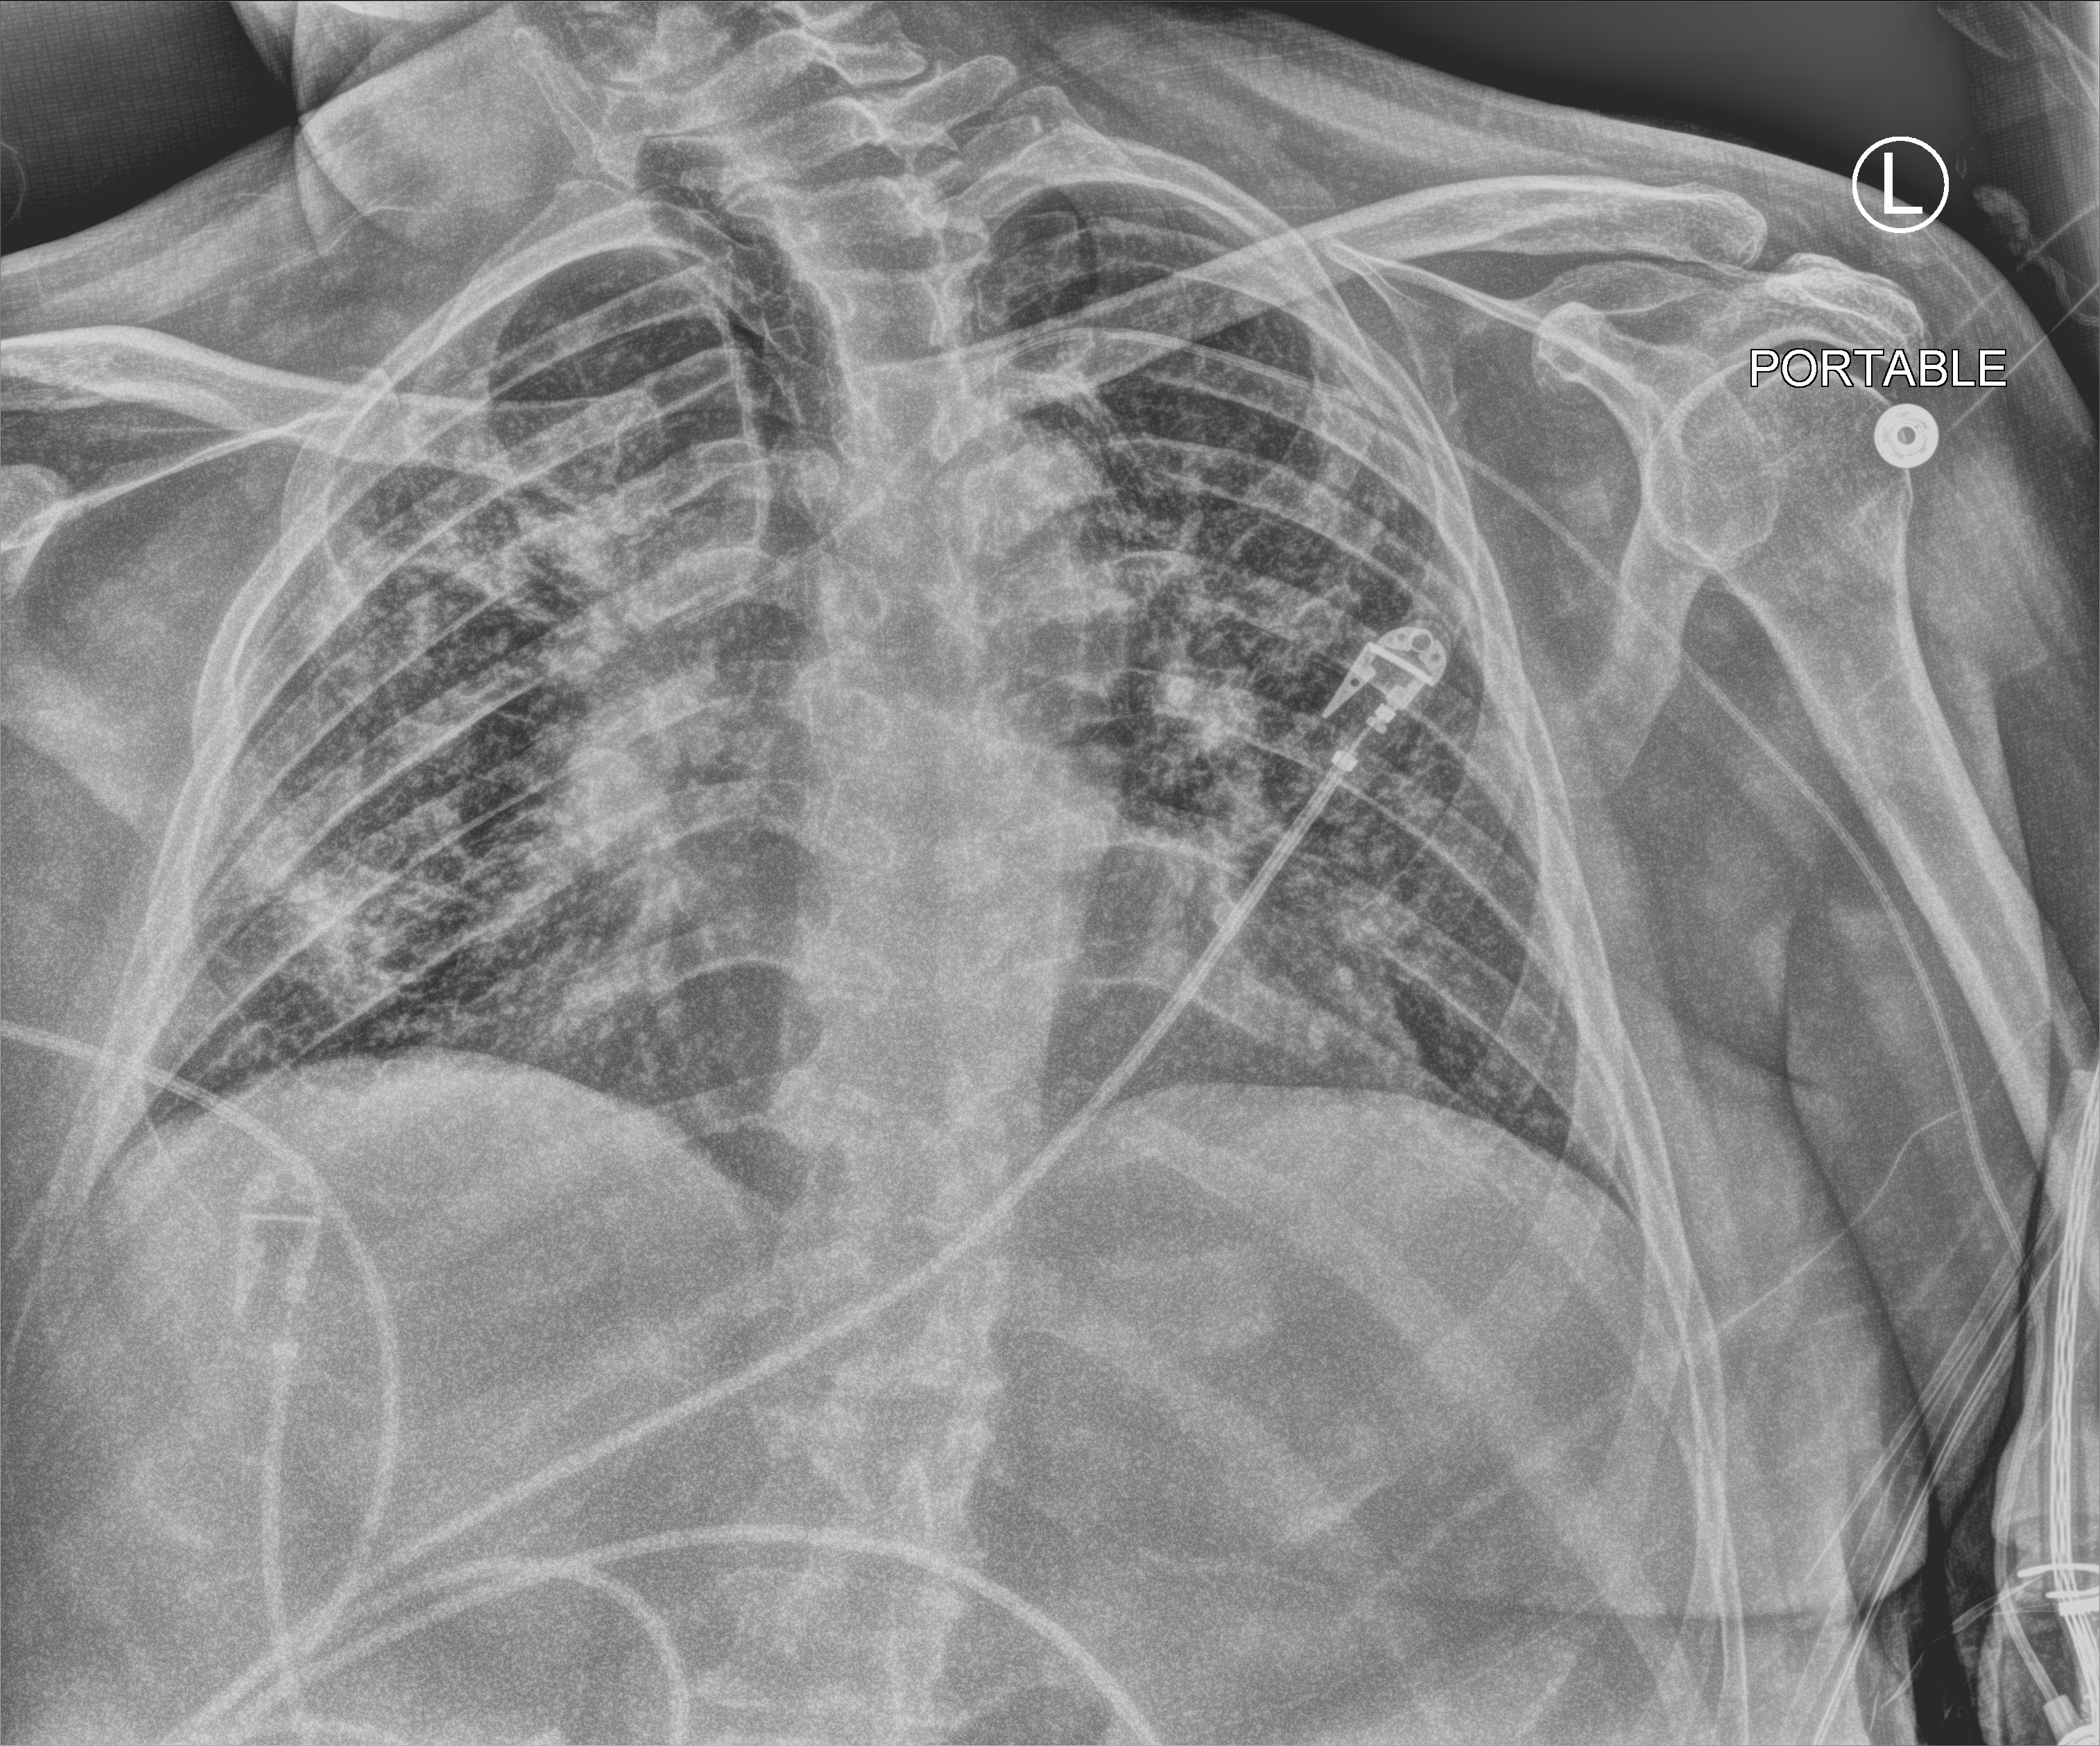
Bedside chest radiograph (computed radiography). Male patient hospitalised with COVID-19, age 18–59 years.
Admission-level facts for this patient (not findings on this image; timing relative to this image not recorded):
- admitted to intensive care during this hospital stay: yes
- mechanically ventilated during this hospital stay: yes